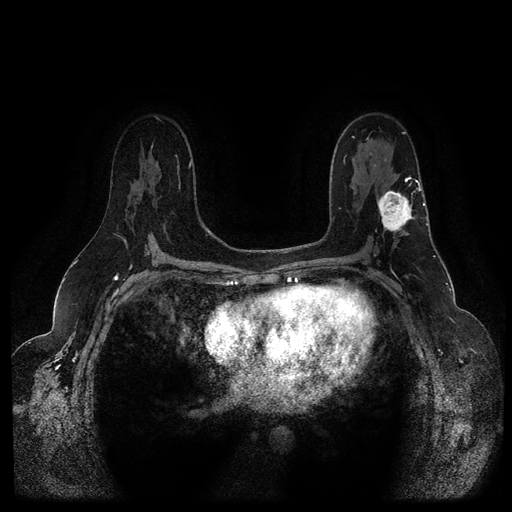
Breast MRI (dynamic contrast-enhanced, multi-phase), one axial slice; position 63 of 116 along the scan axis; dynamic contrast-enhanced series, time point 2 of 5 at this slice position (early post-contrast); 1.5 T; TE 2.6 ms, TR 5.3 ms; 2 mm slice thickness; 512 × 512 image matrix, field of view 350 × 350 mm. Female patient, age 54 years.
Annotated regions visible in this slice (semi-automatically segmented with operator editing):
- breast lesion (labelled 'tumour' in the annotation; benign lesions carry a separate 'benign' label): bounding box <376,189,418,235> (left, top, right, bottom; pixels)